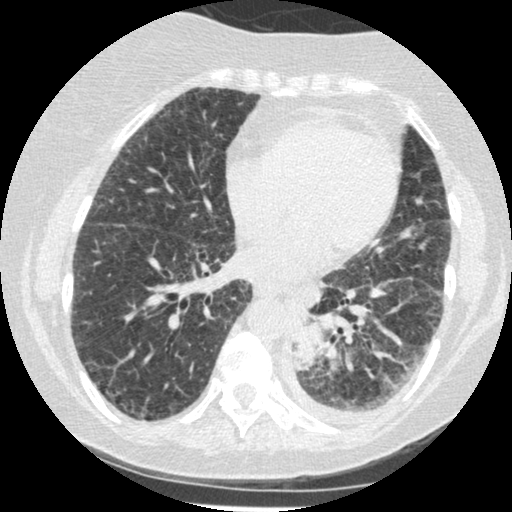
Chest CT (low-dose screening protocol), one axial image. Third annual screen. Lung window (W 1500 / L -600 HU). 1.25 mm slice thickness. Standard (soft-tissue) reconstruction kernel (STANDARD). Slice 260 of 341 in the series. Female participant, aged 60 years at enrolment. Former smoker at enrolment.
Expert-annotated lung lesion, bounding box (x1, y1, x2, y2) in pixels: (279, 301, 344, 376). Reader record for this screening exam (exam-level; its link to the box is not recorded): non-calcified nodule or mass ≥4 mm, left lower lobe, 54 × 38 mm, smooth margins, soft tissue attenuation, pre-existing on the prior screen: yes; interval growth: yes. Participant outcome: lung cancer diagnosed 15 days after this screen — small cell carcinoma, NOS, left lower lobe, undifferentiated (G4), stage IV (AJCC 6th edition), 69 mm at pathology.